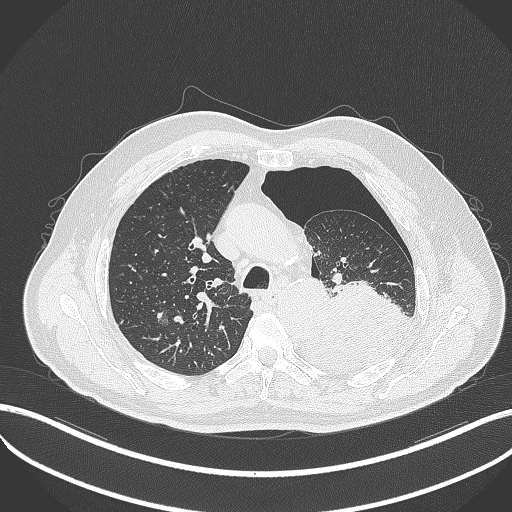
Chest CT, one axial slice. Position 362 of 464 along the scan axis. Reconstruction kernel B70f. 120 kVp. Lung window (W 1500 / L -600 HU). 512 × 512 image matrix, field of view 400 × 400 mm. Patient: male, 76 years. From the clinical record (not read from this slice): clinical TNM (as recorded): T3 N0 M1b.
Annotated regions visible in this slice (rectangle marked by the reading radiologist):
- lung tumour (recorded histology: adenocarcinoma): bounding box [x1, y1, x2, y2] px = [299, 282, 411, 372]